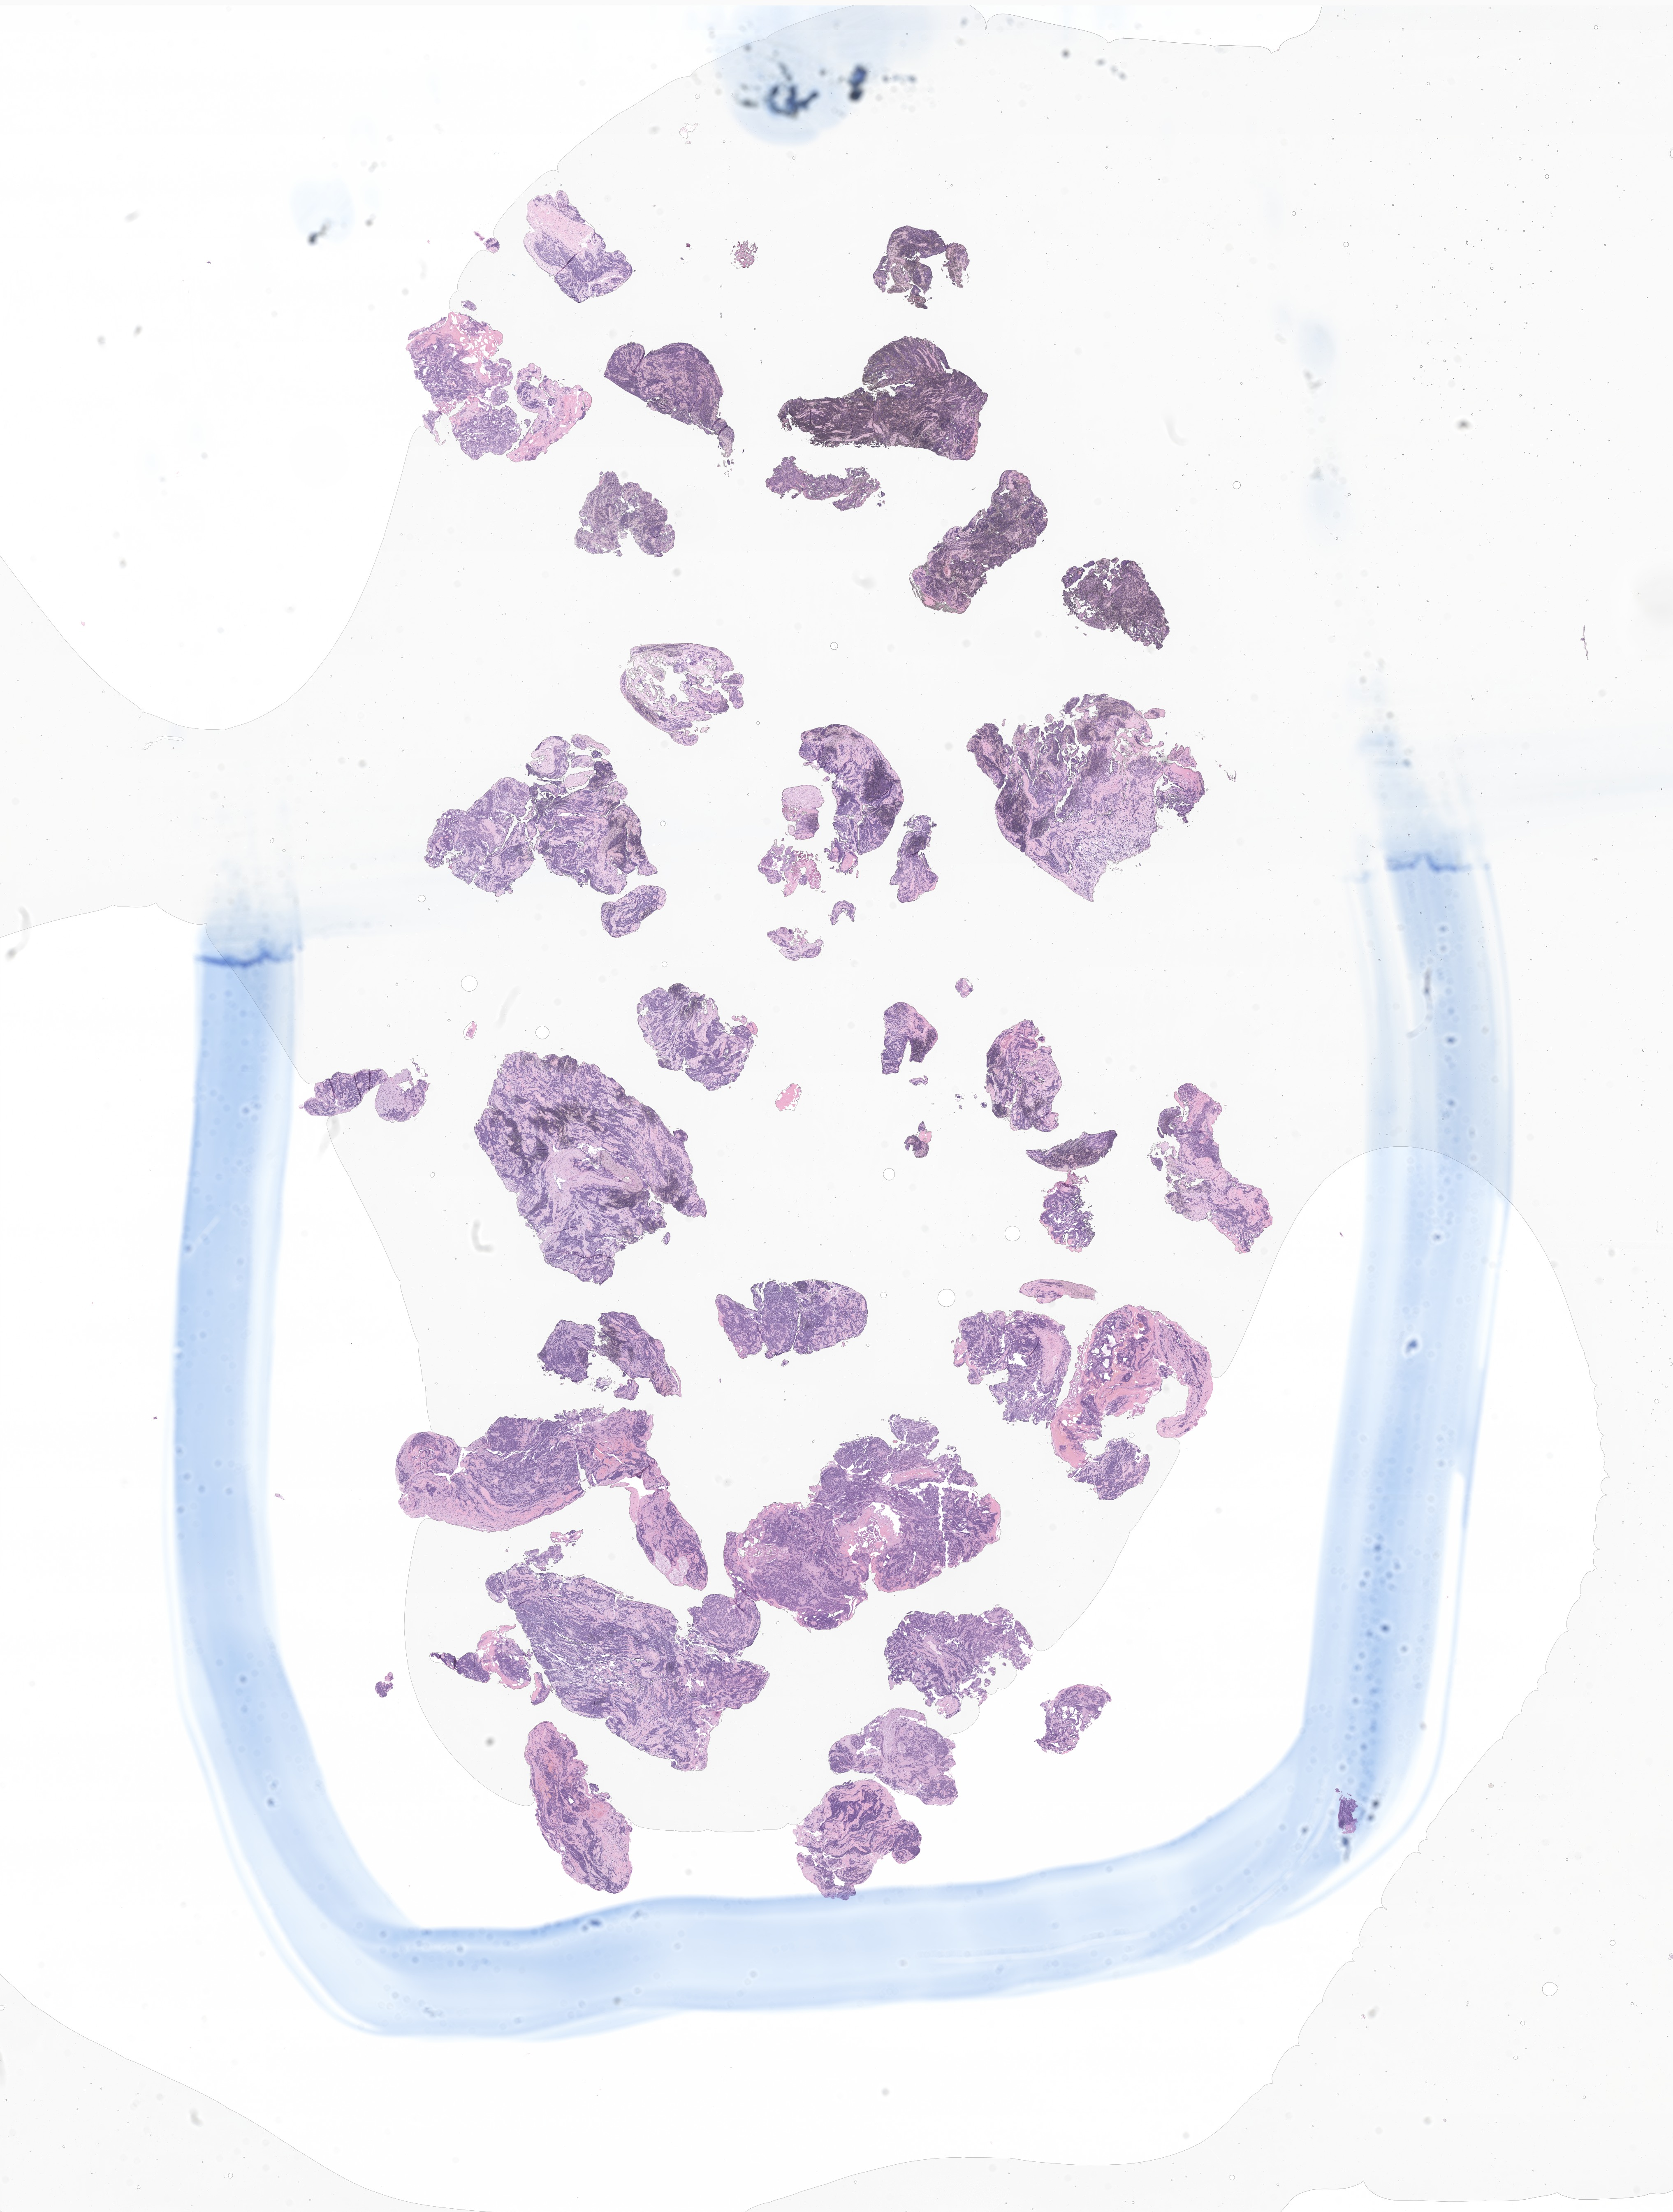
Digitized haematoxylin and eosin-stained section of tumor tissue from the brain — low-resolution overview of the scanned area, about 17.1 x 22.7 mm. Formalin-fixed, paraffin-embedded (FFPE) tissue. Patient male; age 44 months.
Recorded diagnosis: Pineoblastoma.